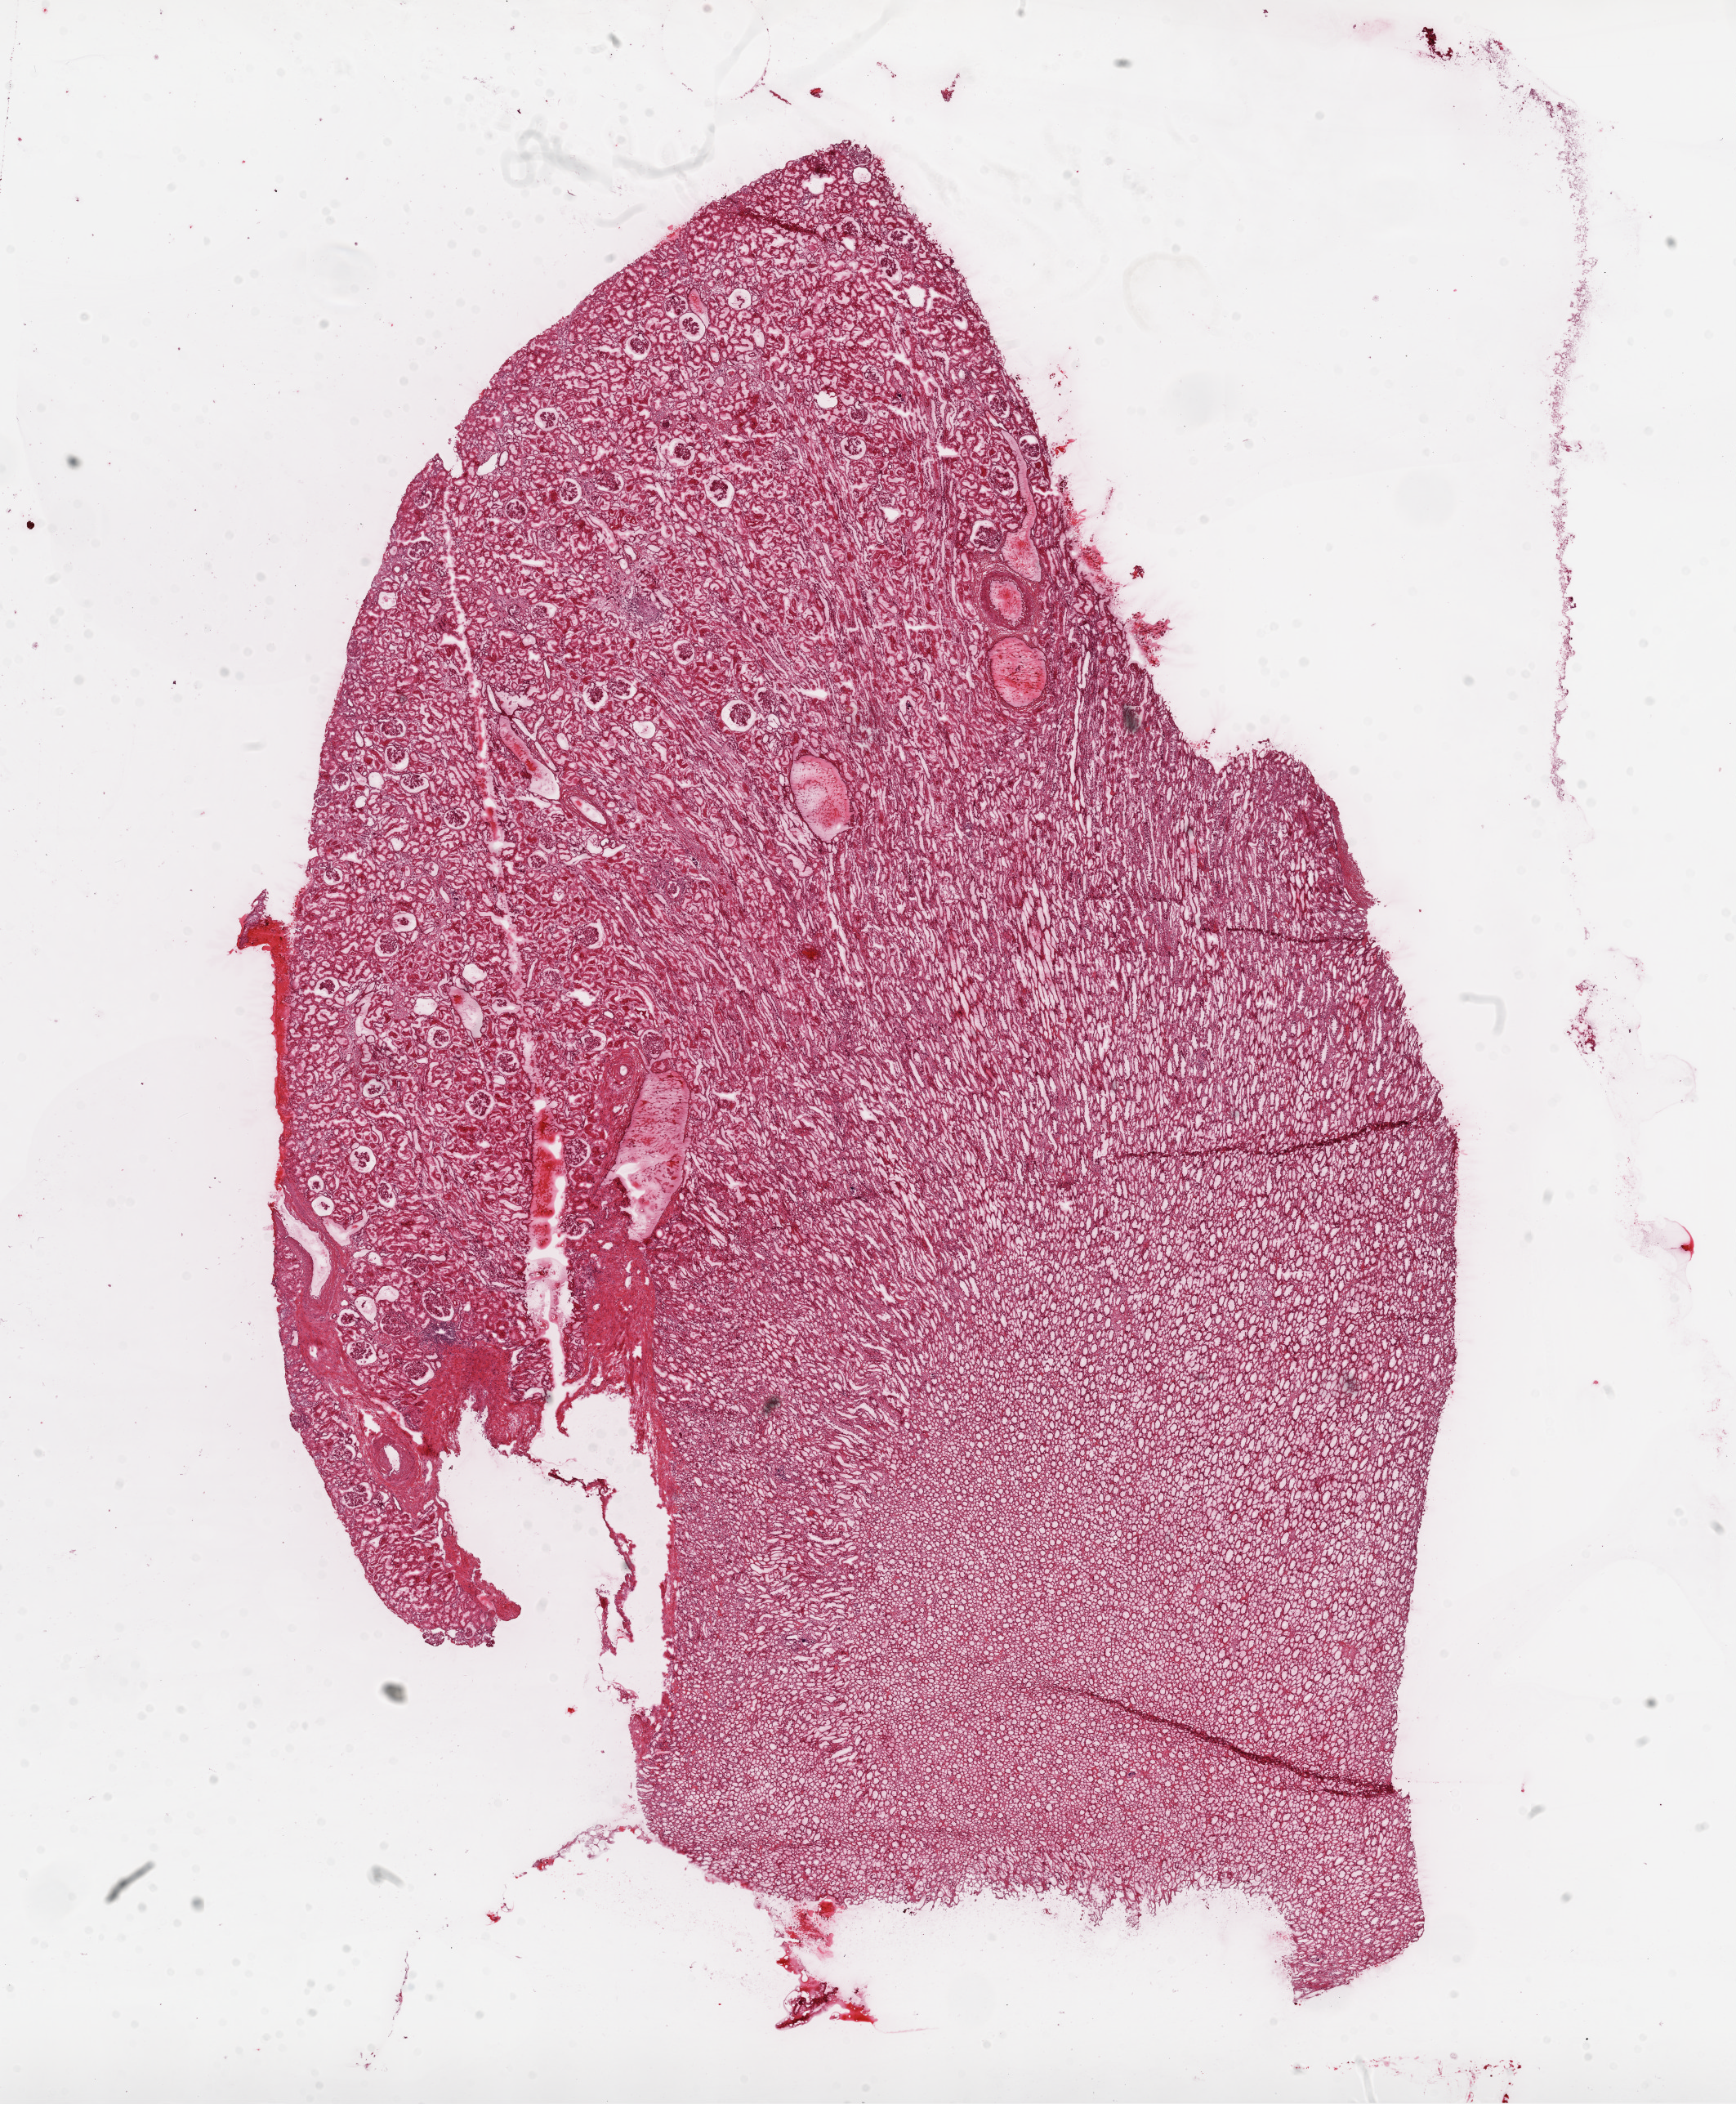
Digitized H&E-stained tissue section (whole slide), a low-resolution overview of the entire scanned area, about 17.1 x 20.7 mm (from a 20x scan); frozen section; sample: solid tissue normal (non-tumour tissue), kidney. Male patient; age at initial diagnosis 47 years.
This section: solid tissue normal (non-tumour) sample from the same patient. Patient diagnosis: Clear cell adenocarcinoma, NOS.